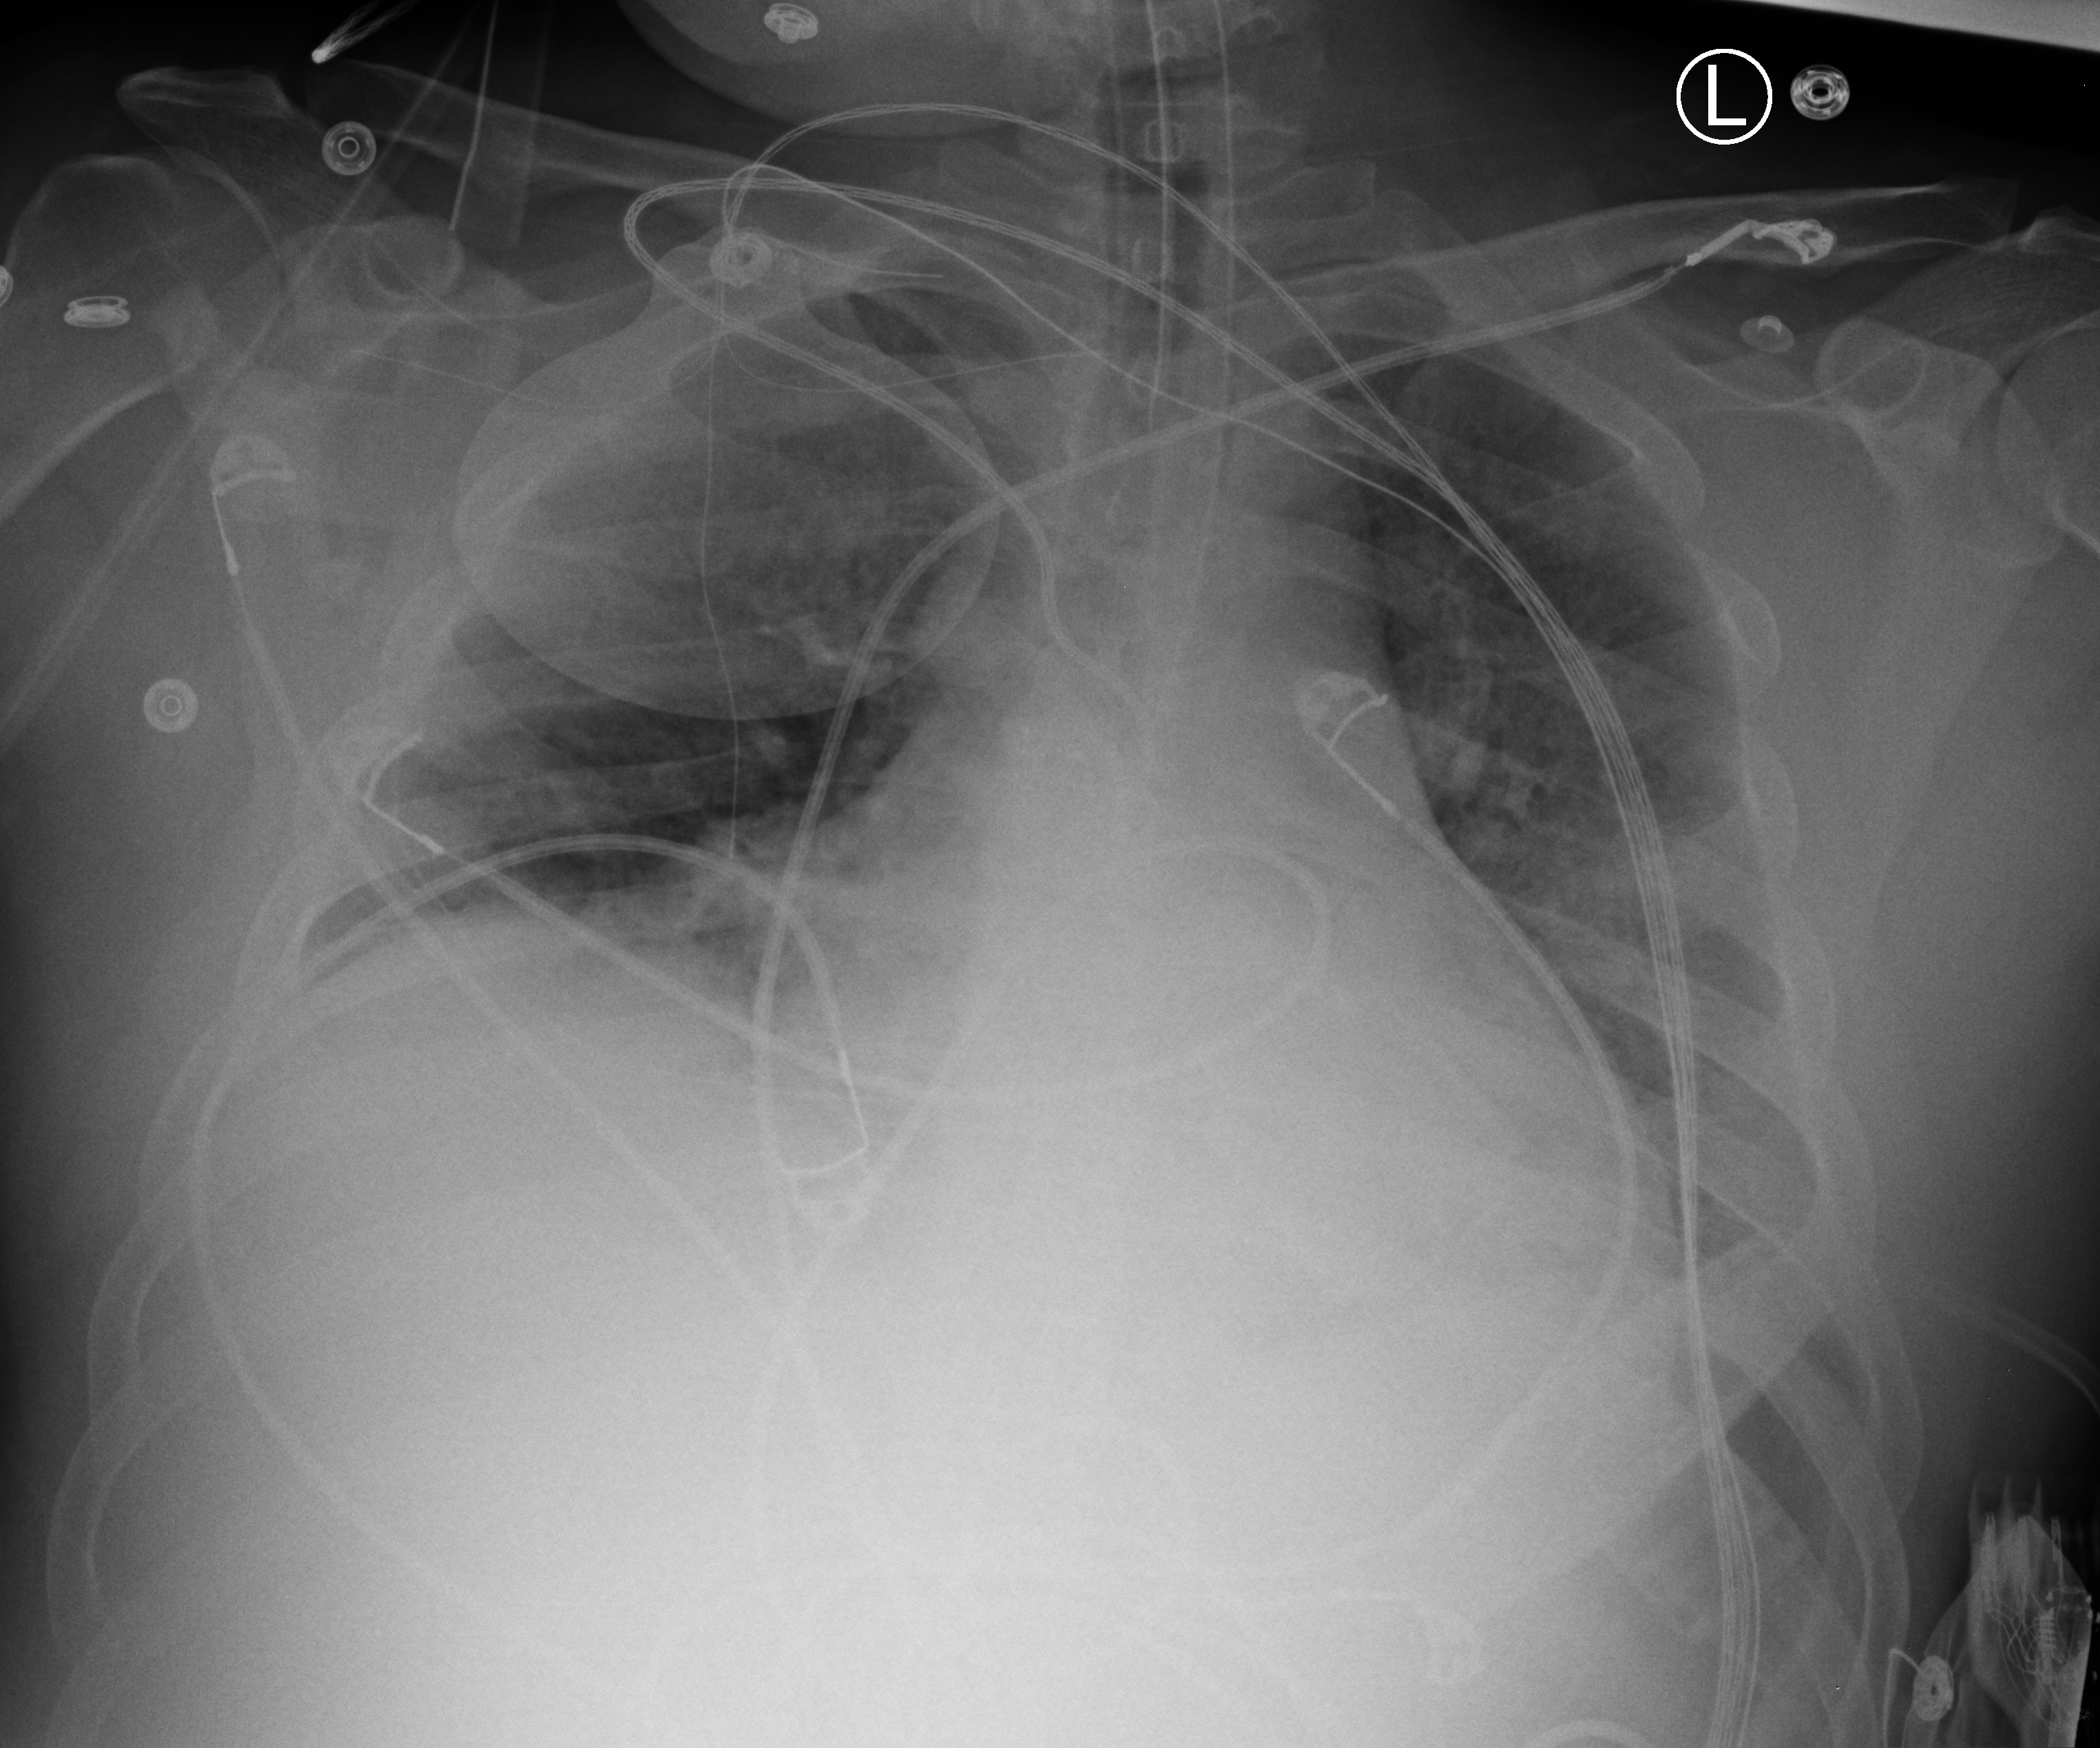
Bedside chest radiograph (computed radiography), anteroposterior (AP) projection. Patient hospitalised with COVID-19; male, aged 18–59 years.
Hospital-stay facts (about this admission, not read from this image; timing relative to this image not recorded): mechanically ventilated during this hospital stay: yes.